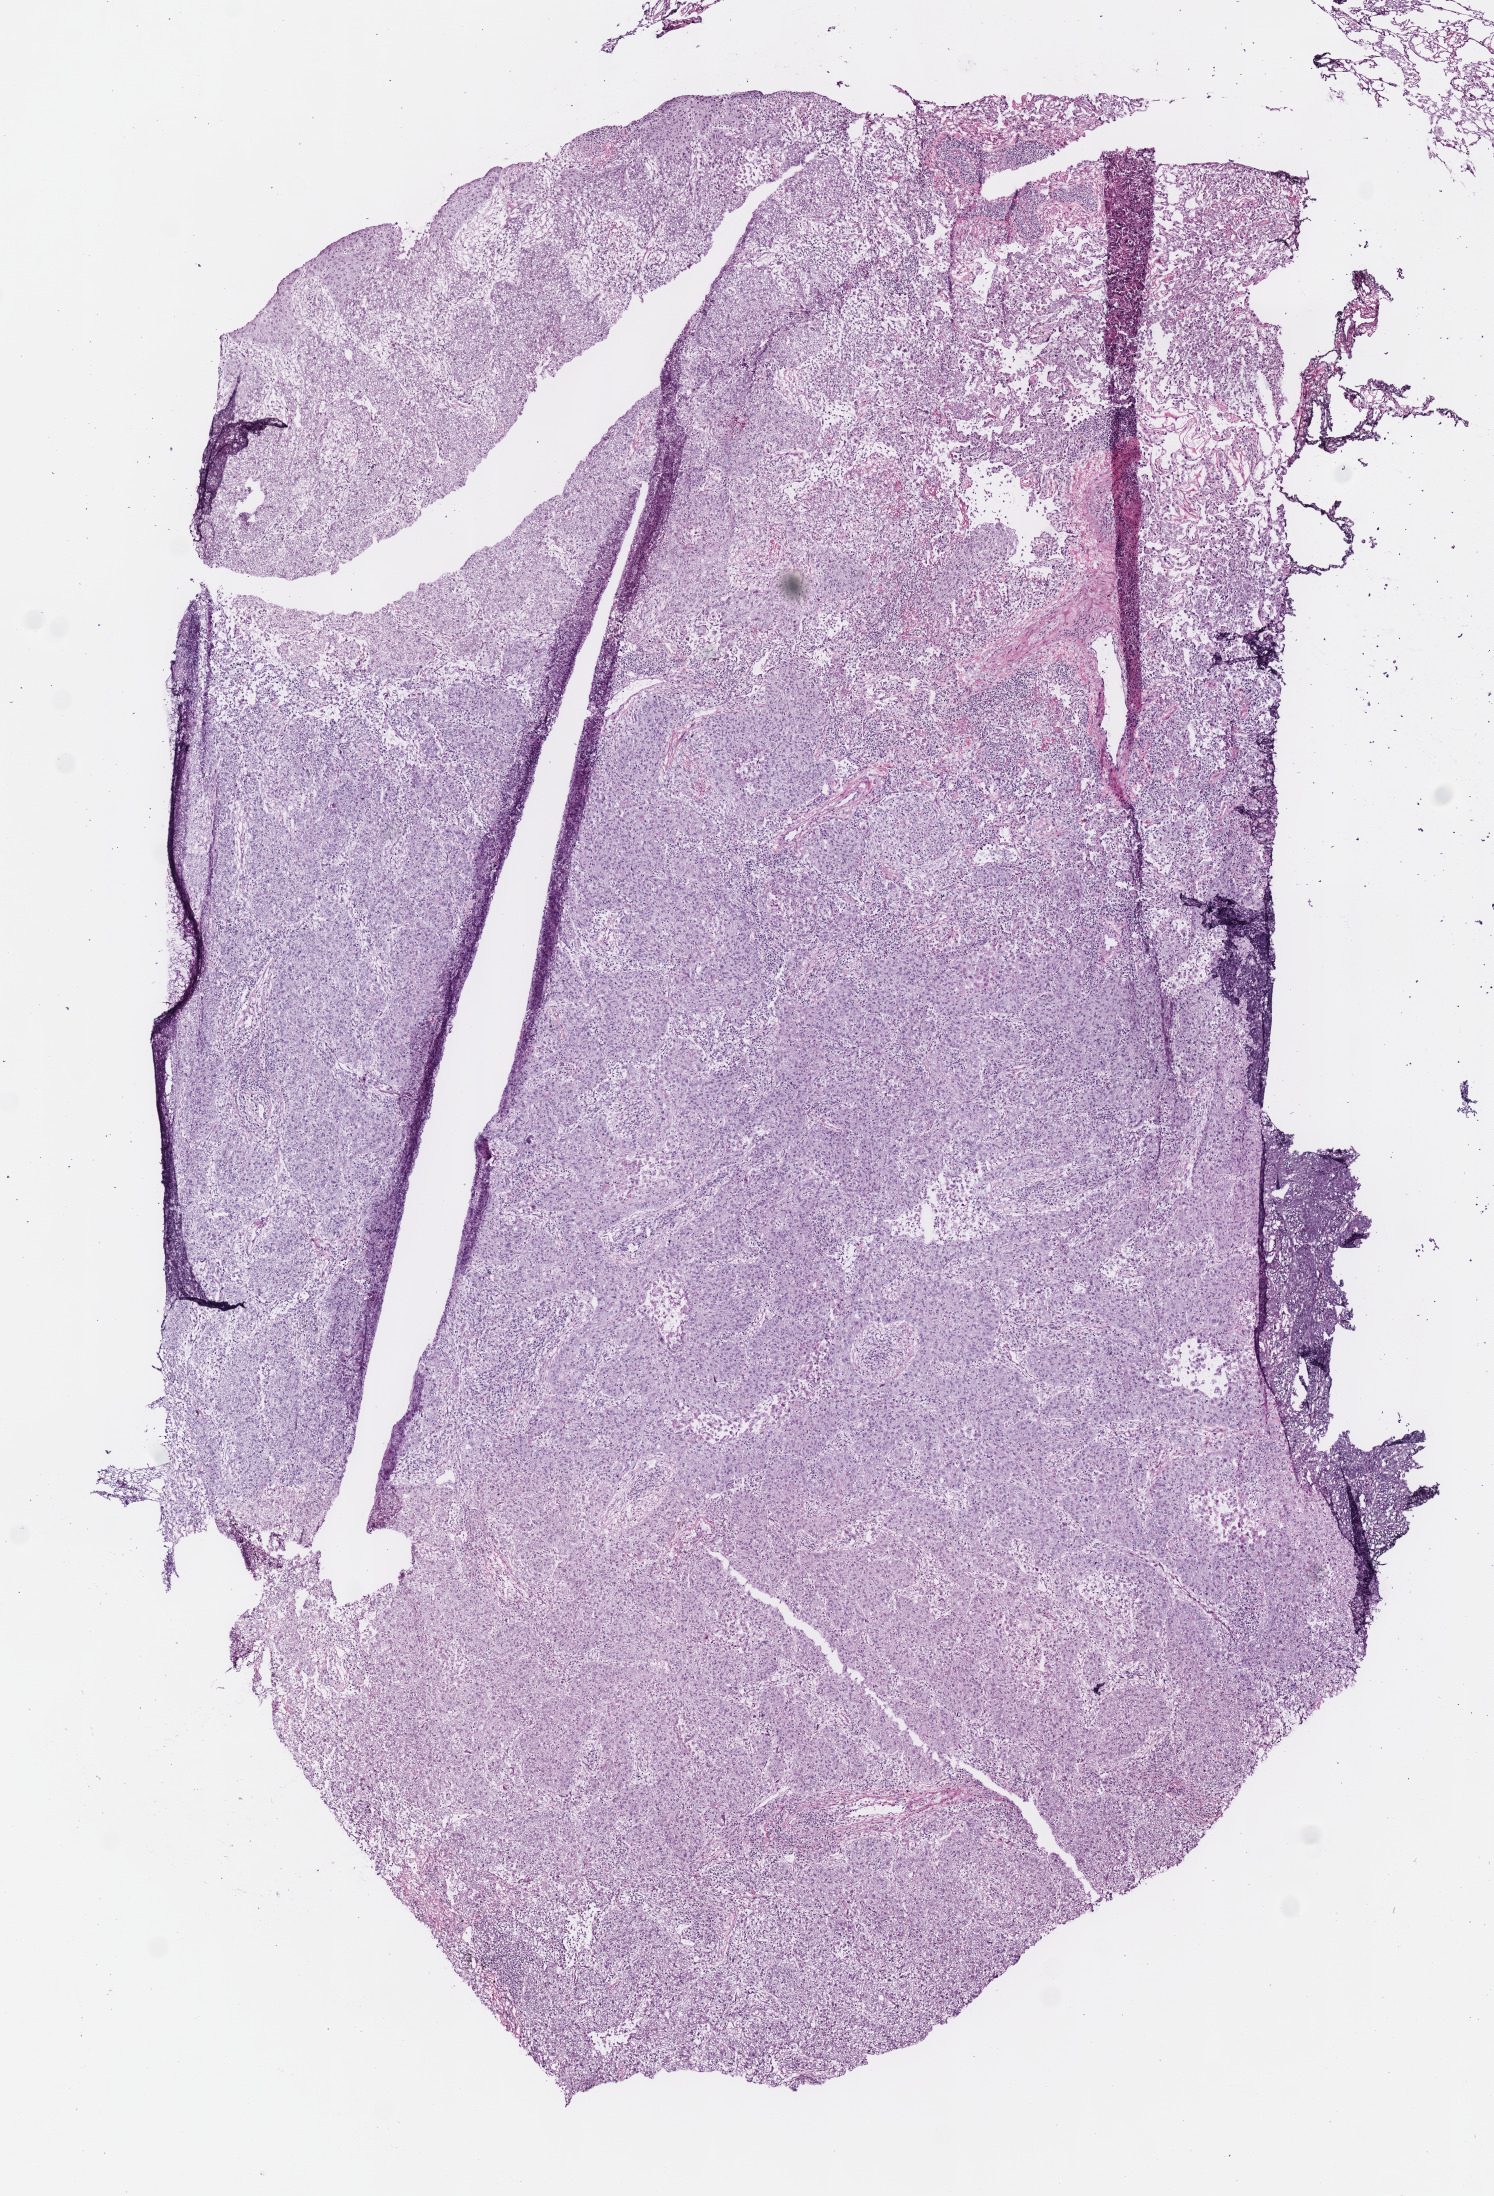
Digitized Hematoxylin and eosin (H&E) stained tissue section (whole slide) — shown as a low-resolution overview of the whole scanned area (about 5.9 x 8.6 mm). Frozen section from the bottom of the tissue portion. Lung, primary tumour sample. Female, age 68 years at initial diagnosis. Composition of this section per pathologist review: tumour cells 85%, tumour nuclei 70%, normal cells 10%, stromal cells 3%, necrosis 2%. Infiltration values recorded for this section: lymphocyte infiltration 15%, monocyte infiltration 3%.
AJCC pathologic stage: IB (7th edition). Laterality: right. Pathologic diagnosis: Squamous cell carcinoma, NOS (lower lobe, lung).